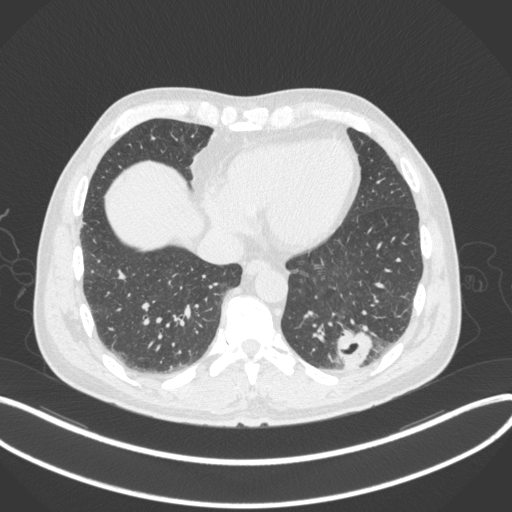
Chest CT, one axial slice; position 79 of 313 along the scan axis; 120 kVp; lung window (W 1500 / L -600 HU); 512 × 512 image matrix, field of view 400 × 400 mm. Patient: male, 54 years. From the clinical record (not read from this slice): clinical TNM (as recorded): T1c N0 M1; histopathological grade: G3.
Outlined on this slice (bounding box drawn by a radiologist):
- lung tumour (recorded histology: adenocarcinoma): box from (x=333, y=321) to (x=374, y=369) px